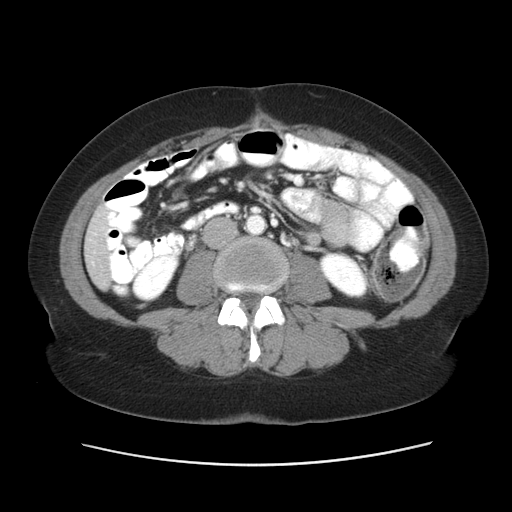
Contrast-enhanced abdominal CT, one axial slice. Position 13 of 52 along the scan axis. 120 kVp. Intravenous contrast given. Soft-tissue window (W 400 / L 40 HU). 5 mm slice thickness. 512 × 512 image matrix. Female patient, age 48 years. From the clinical record (not read from this slice): diagnosis: colorectal cancer liver metastases, imaged before liver resection; multiple liver metastases: yes; largest metastasis: 4.5 cm.
Outlined on this slice (expert manual segmentation):
- liver: bounding box (x1, y1, x2, y2) in pixels: (87, 213, 110, 286)